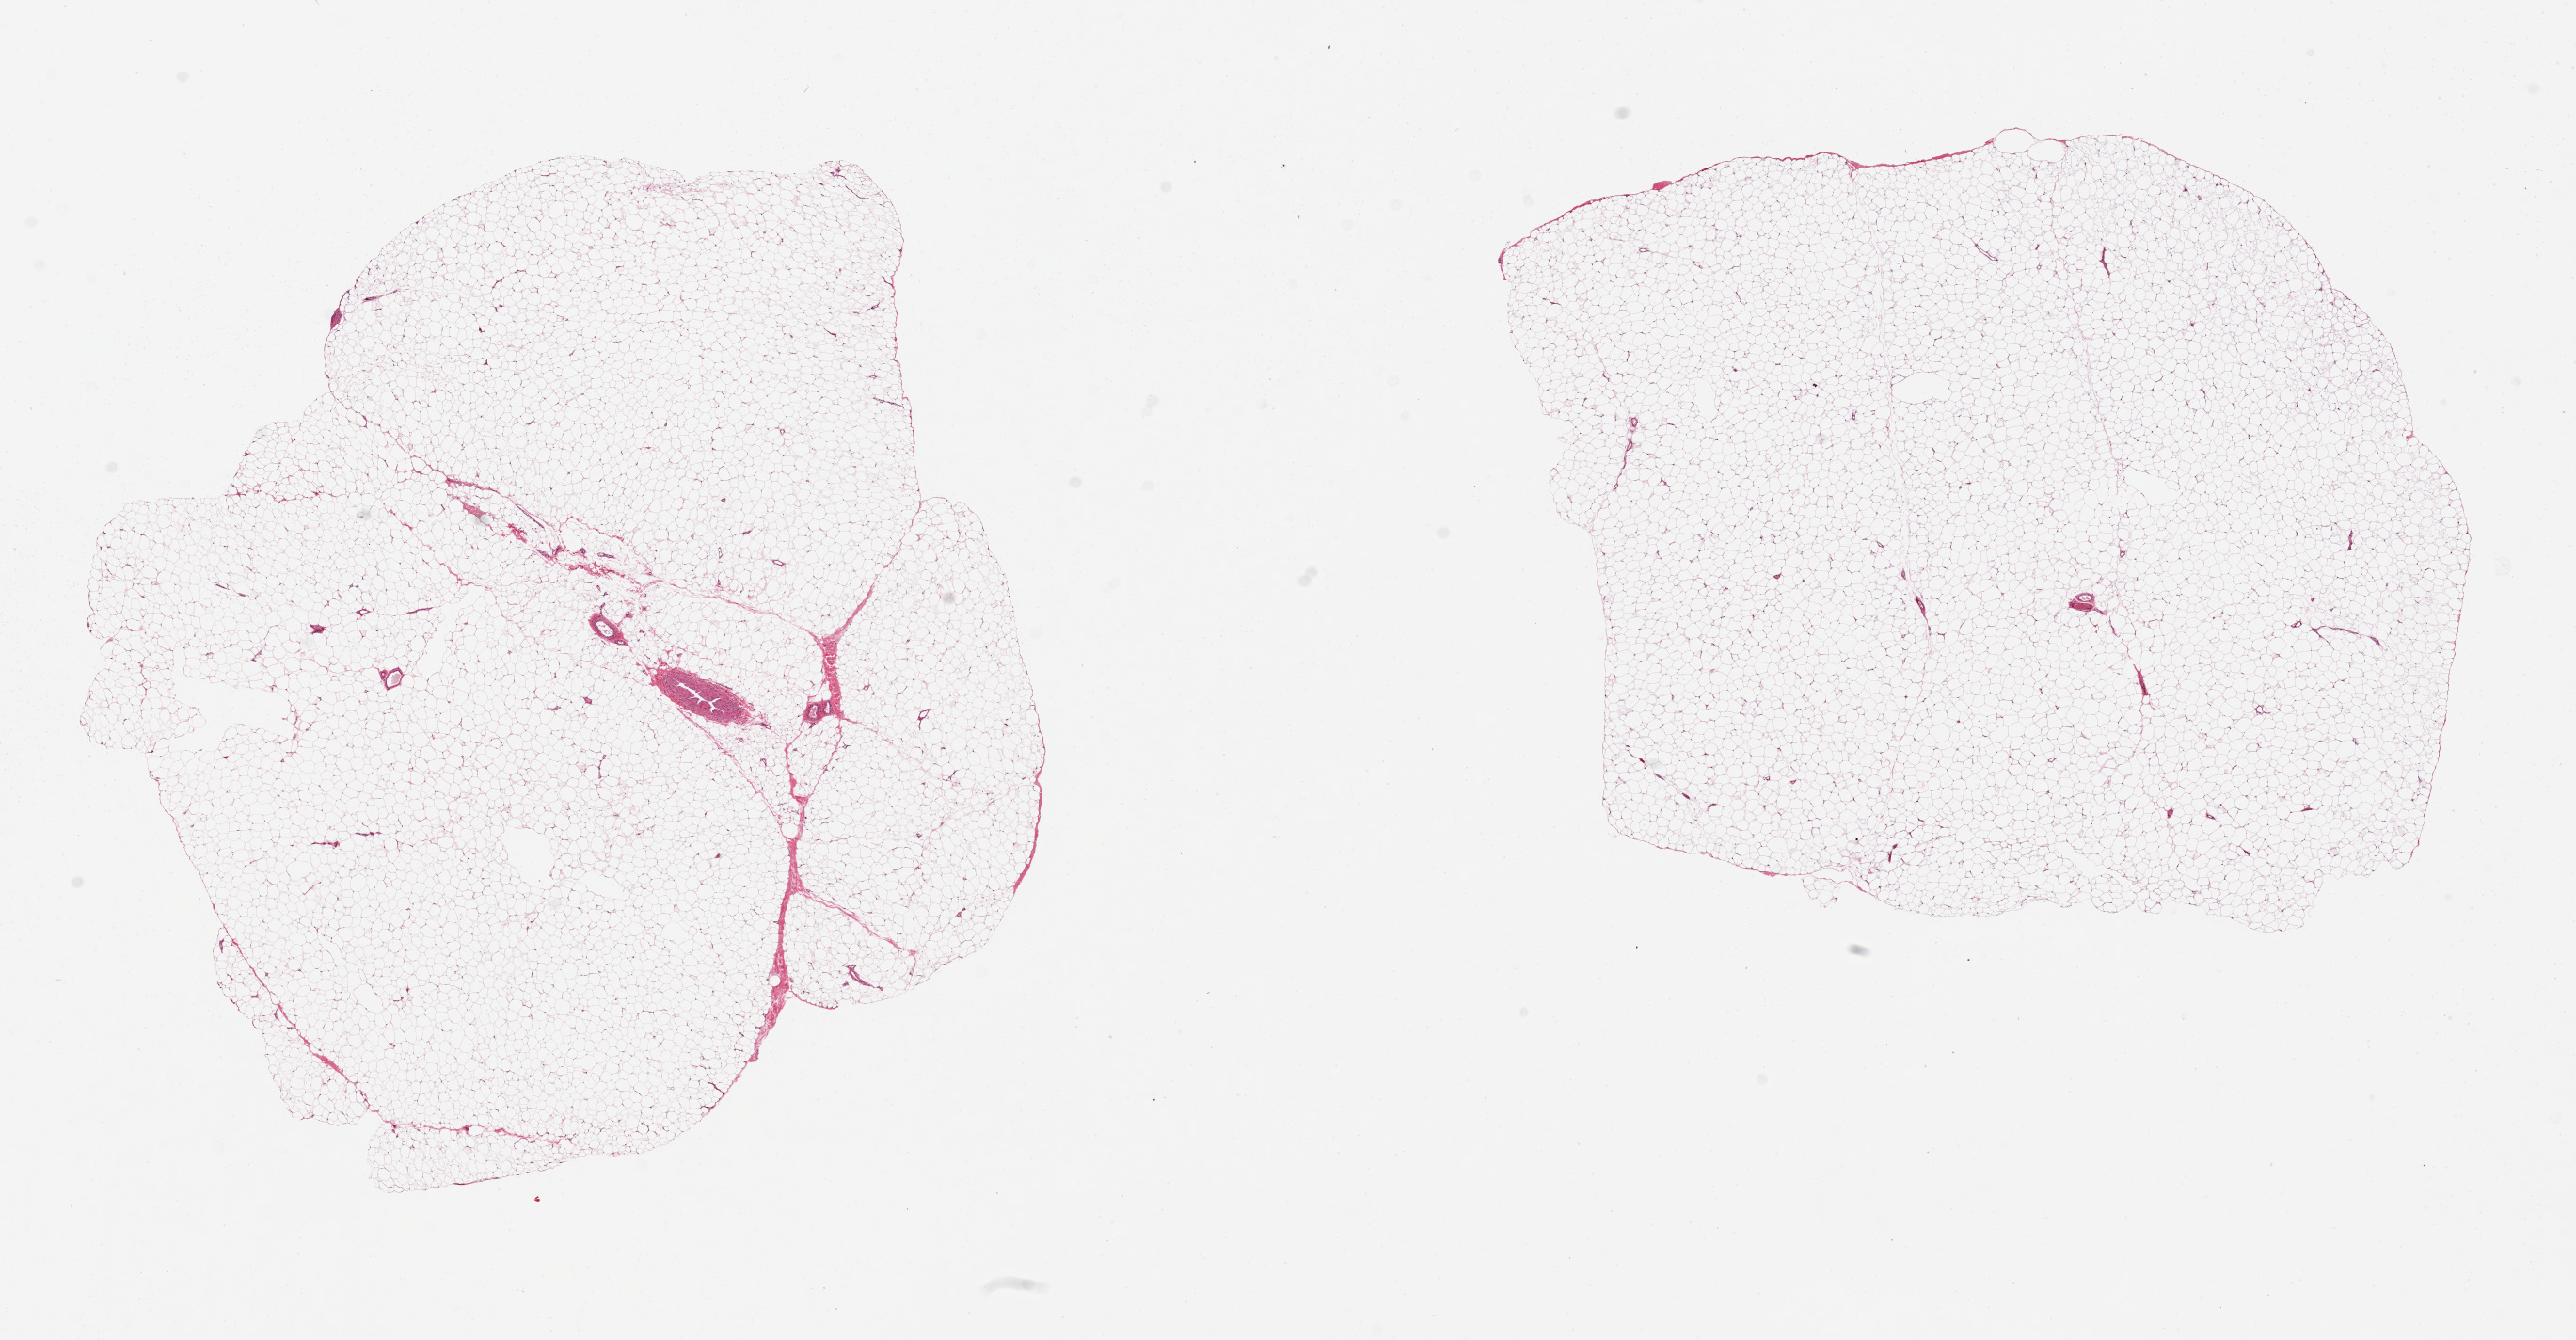
Whole-slide image, hematoxylin and eosin (H&E) stain, shown as a low-resolution overview of the whole scanned area (about 21.7 x 11.3 mm); PAXgene-fixed, paraffin-embedded tissue; section of adipose tissue (target tissue); tissue donor sample. Male donor.
Reviewer comment on this tissue sample: 2 pieces, 9.5x8 & 8x7mm.